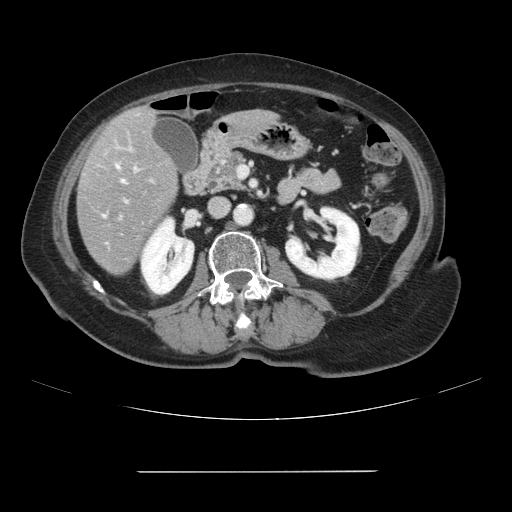
Contrast-enhanced abdominal CT, one axial slice; slice 31 of 111 in the series (ordered by position); 120 kVp; intravenous contrast given; soft-tissue window (W 400 / L 40 HU); 2.5 mm slice thickness; 512 × 512 image matrix. Female patient, age 74 years. From the clinical record (not read from this slice): diagnosis: colorectal cancer liver metastases, imaged before liver resection; multiple liver metastases: yes; largest metastasis: 1.1 cm; disease in both lobes: yes.
Annotated regions visible in this slice (expert manual segmentation):
- hepatic veins: bounding box <117,166,125,183> (left, top, right, bottom; pixels)
- liver: <78,107,177,275>
- planned liver remnant (the part of the liver to remain after resection): <141,108,156,123>